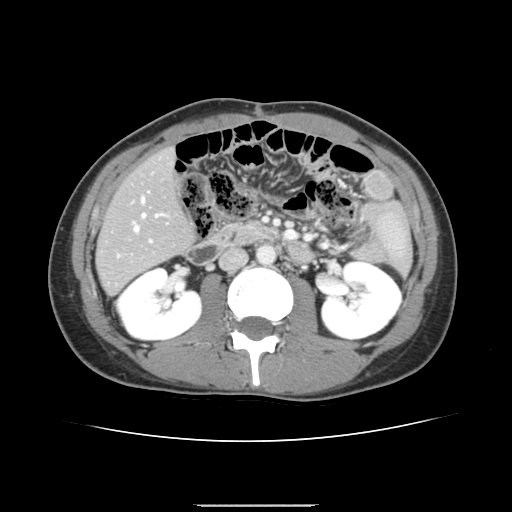
Contrast-enhanced abdominal CT, one axial slice. Slice 61 of 150 in the series (ordered by position). Intravenous contrast given. Soft-tissue window (W 400 / L 40 HU). 512 × 512 image matrix, field of view 324 × 324 mm. Female patient, age 32 years. From the clinical record (not read from this slice): diagnosis: colorectal cancer liver metastases, imaged before liver resection; multiple liver metastases: yes; largest metastasis: 0.7 cm; disease in both lobes: no.
Outlined on this slice (expert manual segmentation):
- hepatic veins: bounding box [x1, y1, x2, y2] px = [134, 197, 162, 231]
- liver: [98, 149, 193, 294]
- planned liver remnant (the part of the liver to remain after resection): [98, 149, 193, 293]
- portal vein (with intrahepatic branches): [118, 191, 152, 256]